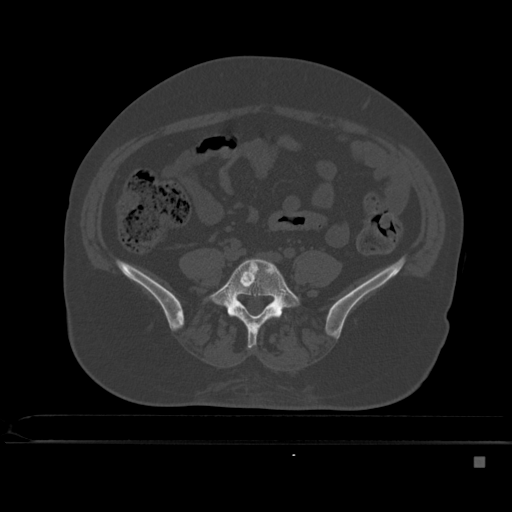
CT including the spine, one axial slice; slice 110 of 495 in the series (ordered by position); bone window (W 1800 / L 400 HU); 1.5 mm slice thickness; 512 × 512 image matrix, field of view 404 × 404 mm. Patient: female, 33 years. Case-level facts recorded for this patient, not image findings: primary cancer: breast; vertebrae with lytic lesions (as recorded): T1.
Annotated regions visible in this slice (semi-automatically segmented with operator editing):
- L5 vertebra: bounding box [x1, y1, x2, y2] px = [203, 258, 300, 348]